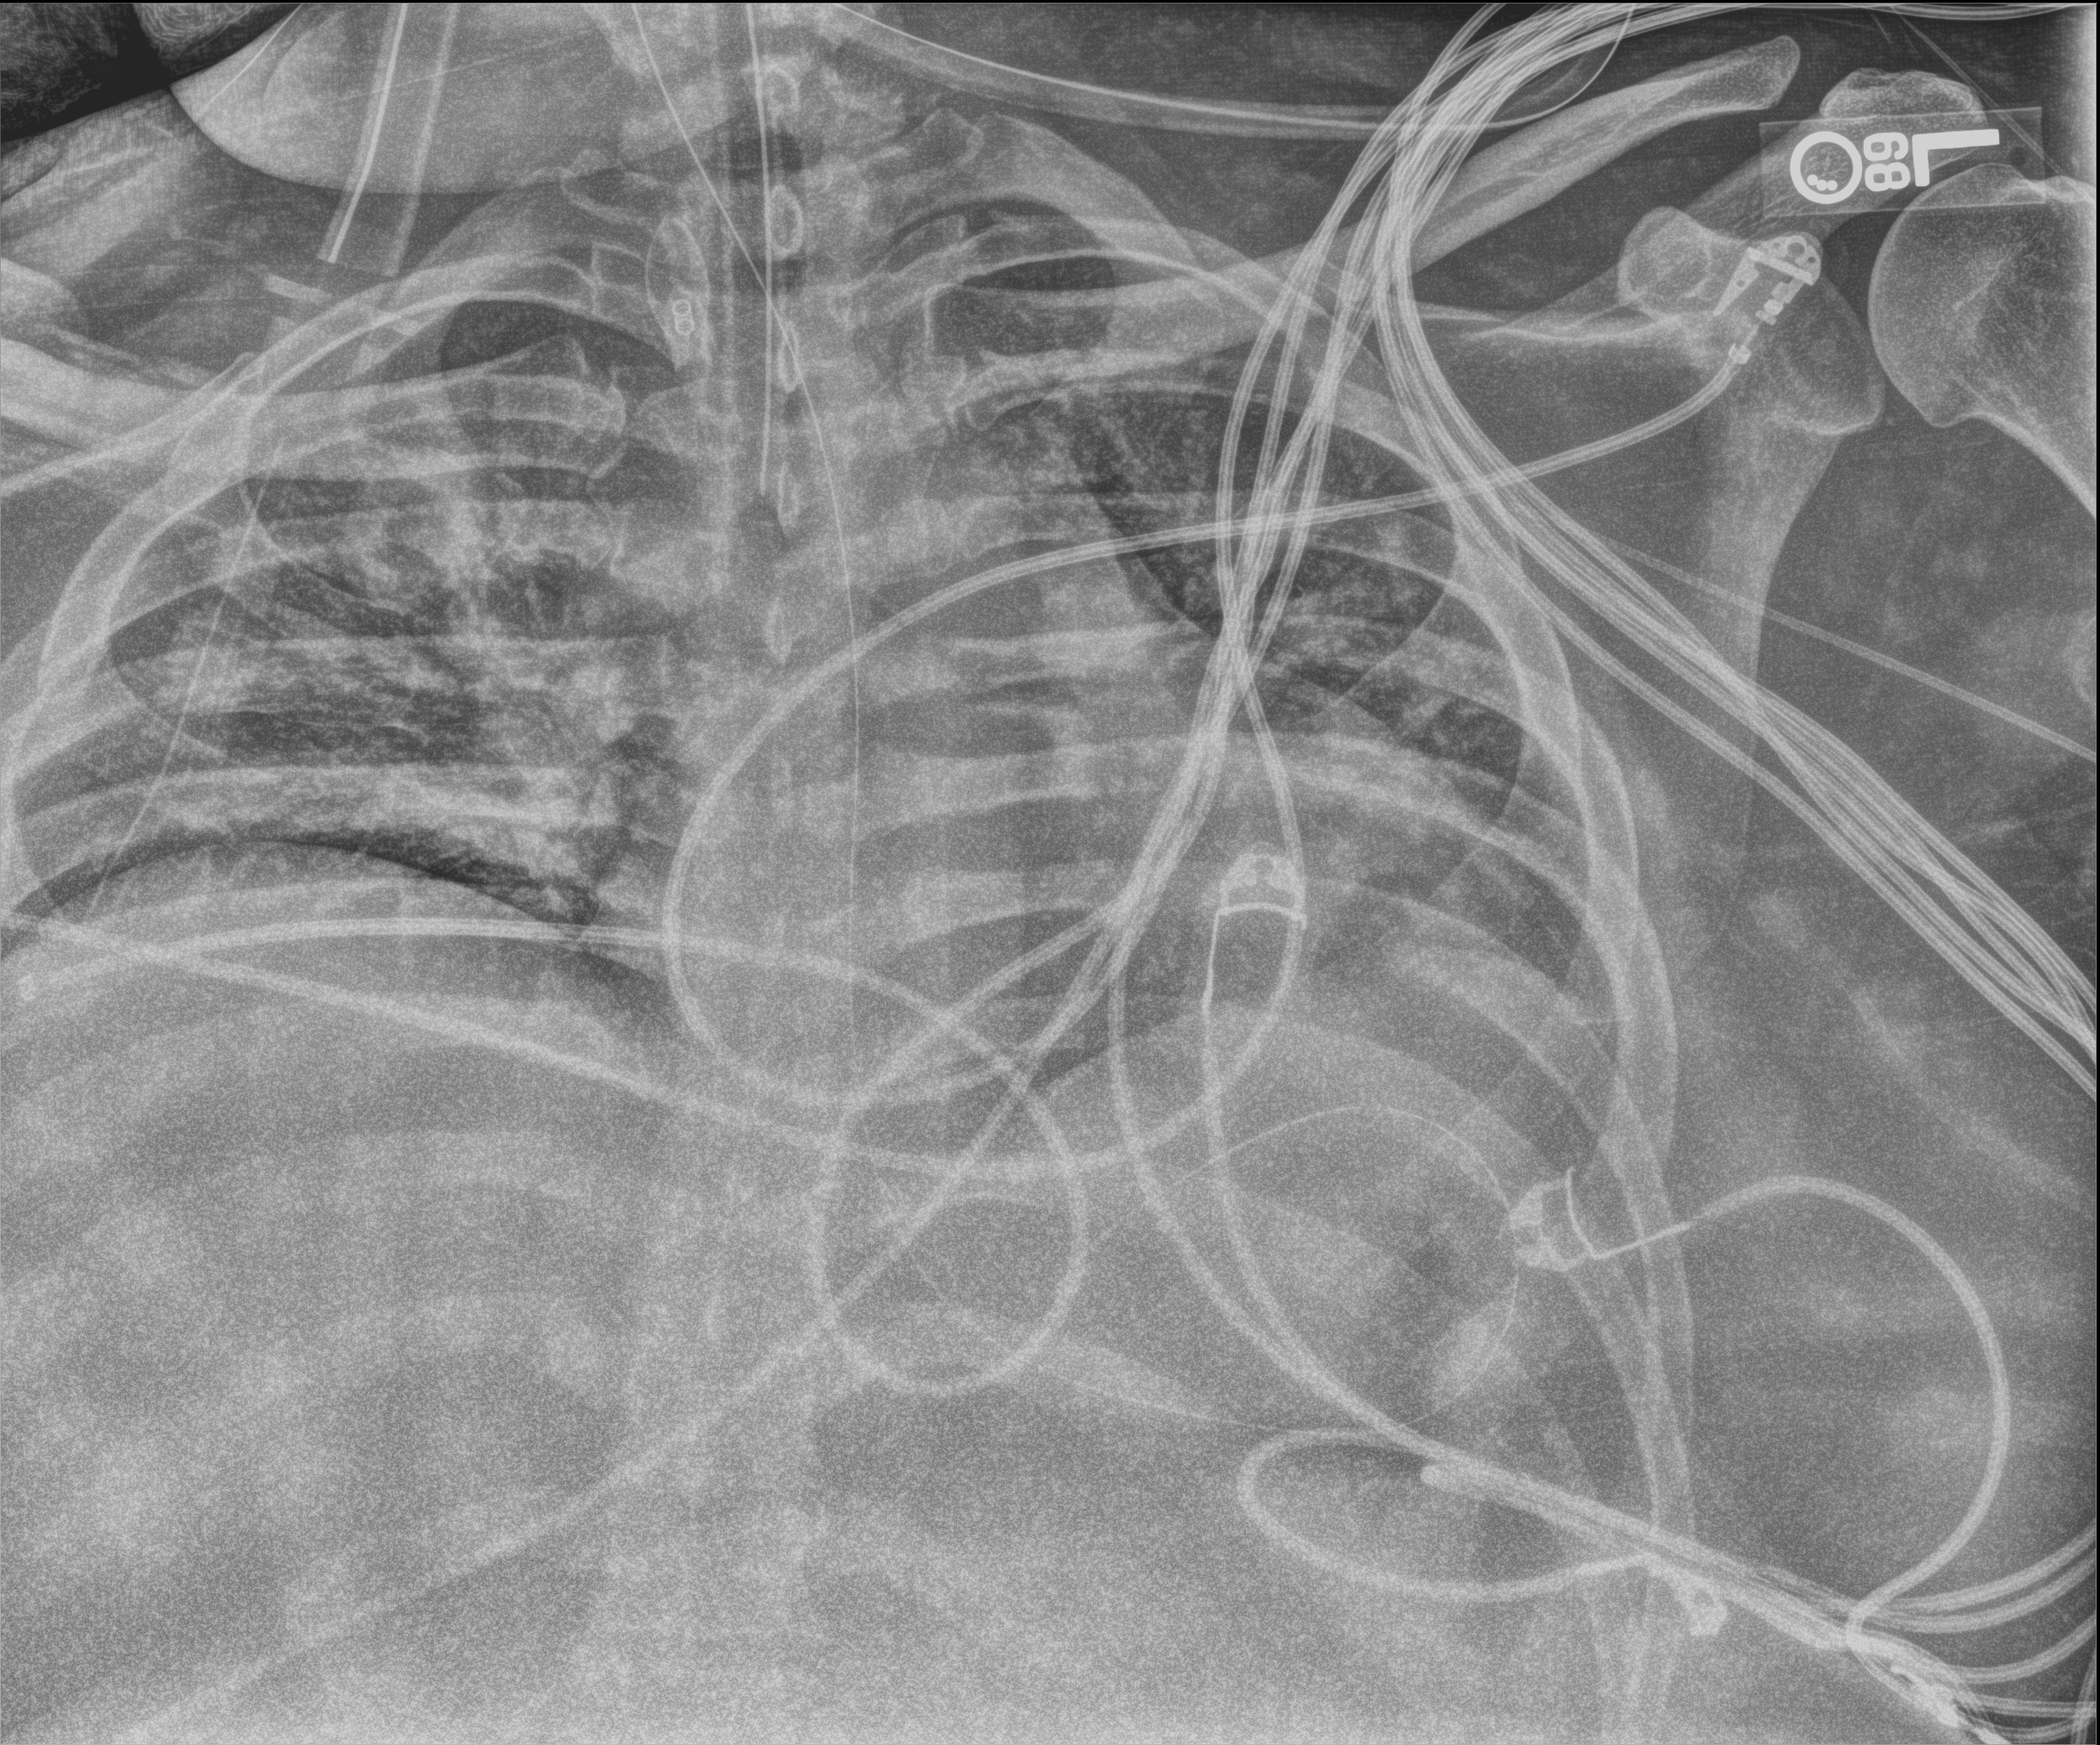
Portable chest radiograph. Patient hospitalised with COVID-19; male, aged 18–59 years.
From the hospital-stay record, not from the radiograph (when in the stay this image was taken is not recorded):
- COPD (admission record): yes